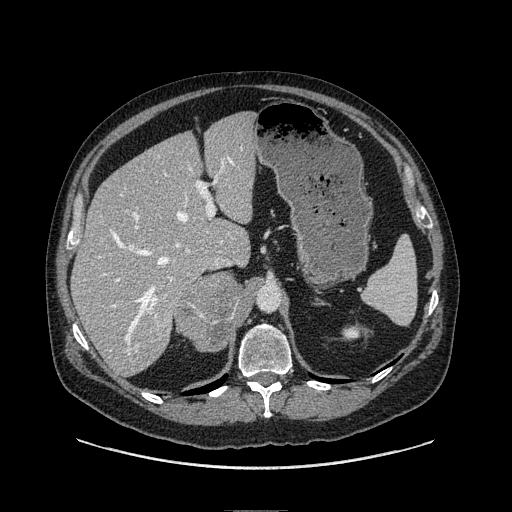
Contrast-enhanced abdominal CT, one axial slice. Position 65 of 149 along the scan axis. Soft-tissue window (W 400 / L 40 HU). 1.25 mm slice thickness. 512 × 512 image matrix, field of view 440 × 440 mm. Male patient. From the clinical record (not read from this slice): diagnosis: adrenocortical carcinoma; tumour side: right adrenal; tumour size at pathology: 7.5 cm; Ki-67 index: 15 %; stage (as recorded): 2.
Annotated regions visible in this slice (semi-automatically segmented with operator editing):
- mass: box from (x=175, y=272) to (x=249, y=348) px